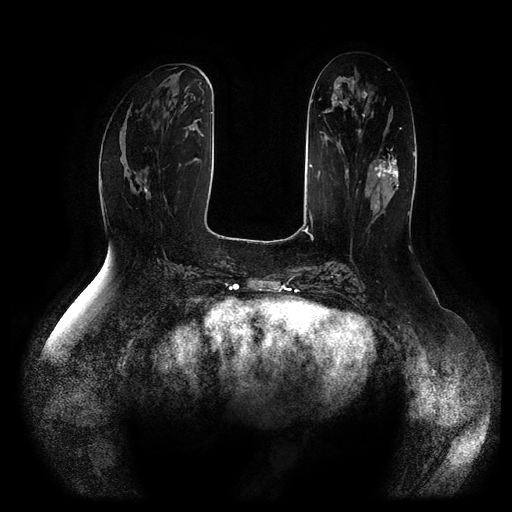
Breast MRI (dynamic contrast-enhanced, multi-phase), one axial slice; position 38 of 116 along the scan axis; dynamic contrast-enhanced series, time point 2 of 5 at this slice position (early post-contrast); 1.5 T; TE 2.5 ms, TR 5.2 ms; 2 mm slice thickness; 512 × 512 image matrix, field of view 400 × 400 mm. Female patient, age 66 years.
Structures marked on this image (semi-automatic segmentation, software-assisted and operator-edited):
- breast lesion (labelled 'tumour' in the annotation; benign lesions carry a separate 'benign' label): bounding box <374,147,399,193> (left, top, right, bottom; pixels)